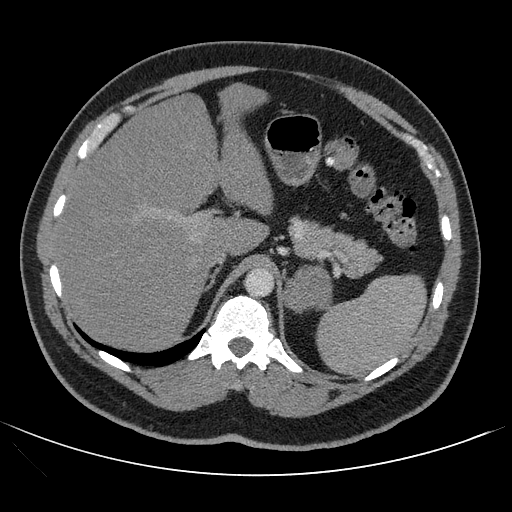
Contrast-enhanced abdominal CT, one axial slice; slice 78 of 121 in the series (ordered by position); 120 kVp; intravenous contrast given; soft-tissue window (W 400 / L 40 HU); 2.5 mm slice thickness; 512 × 512 image matrix, field of view 399 × 399 mm. Male patient, age 53 years. Case-level facts recorded for this patient, not image findings: diagnosis: adrenocortical carcinoma; tumour side: left adrenal; tumour size at pathology: 7.9 cm; Ki-67 index: 20 %; stage (as recorded): 2.
Outlined on this slice (semi-automatic segmentation, software-assisted and operator-edited):
- mass: bounding box (x1, y1, x2, y2) in pixels: (283, 266, 331, 312)